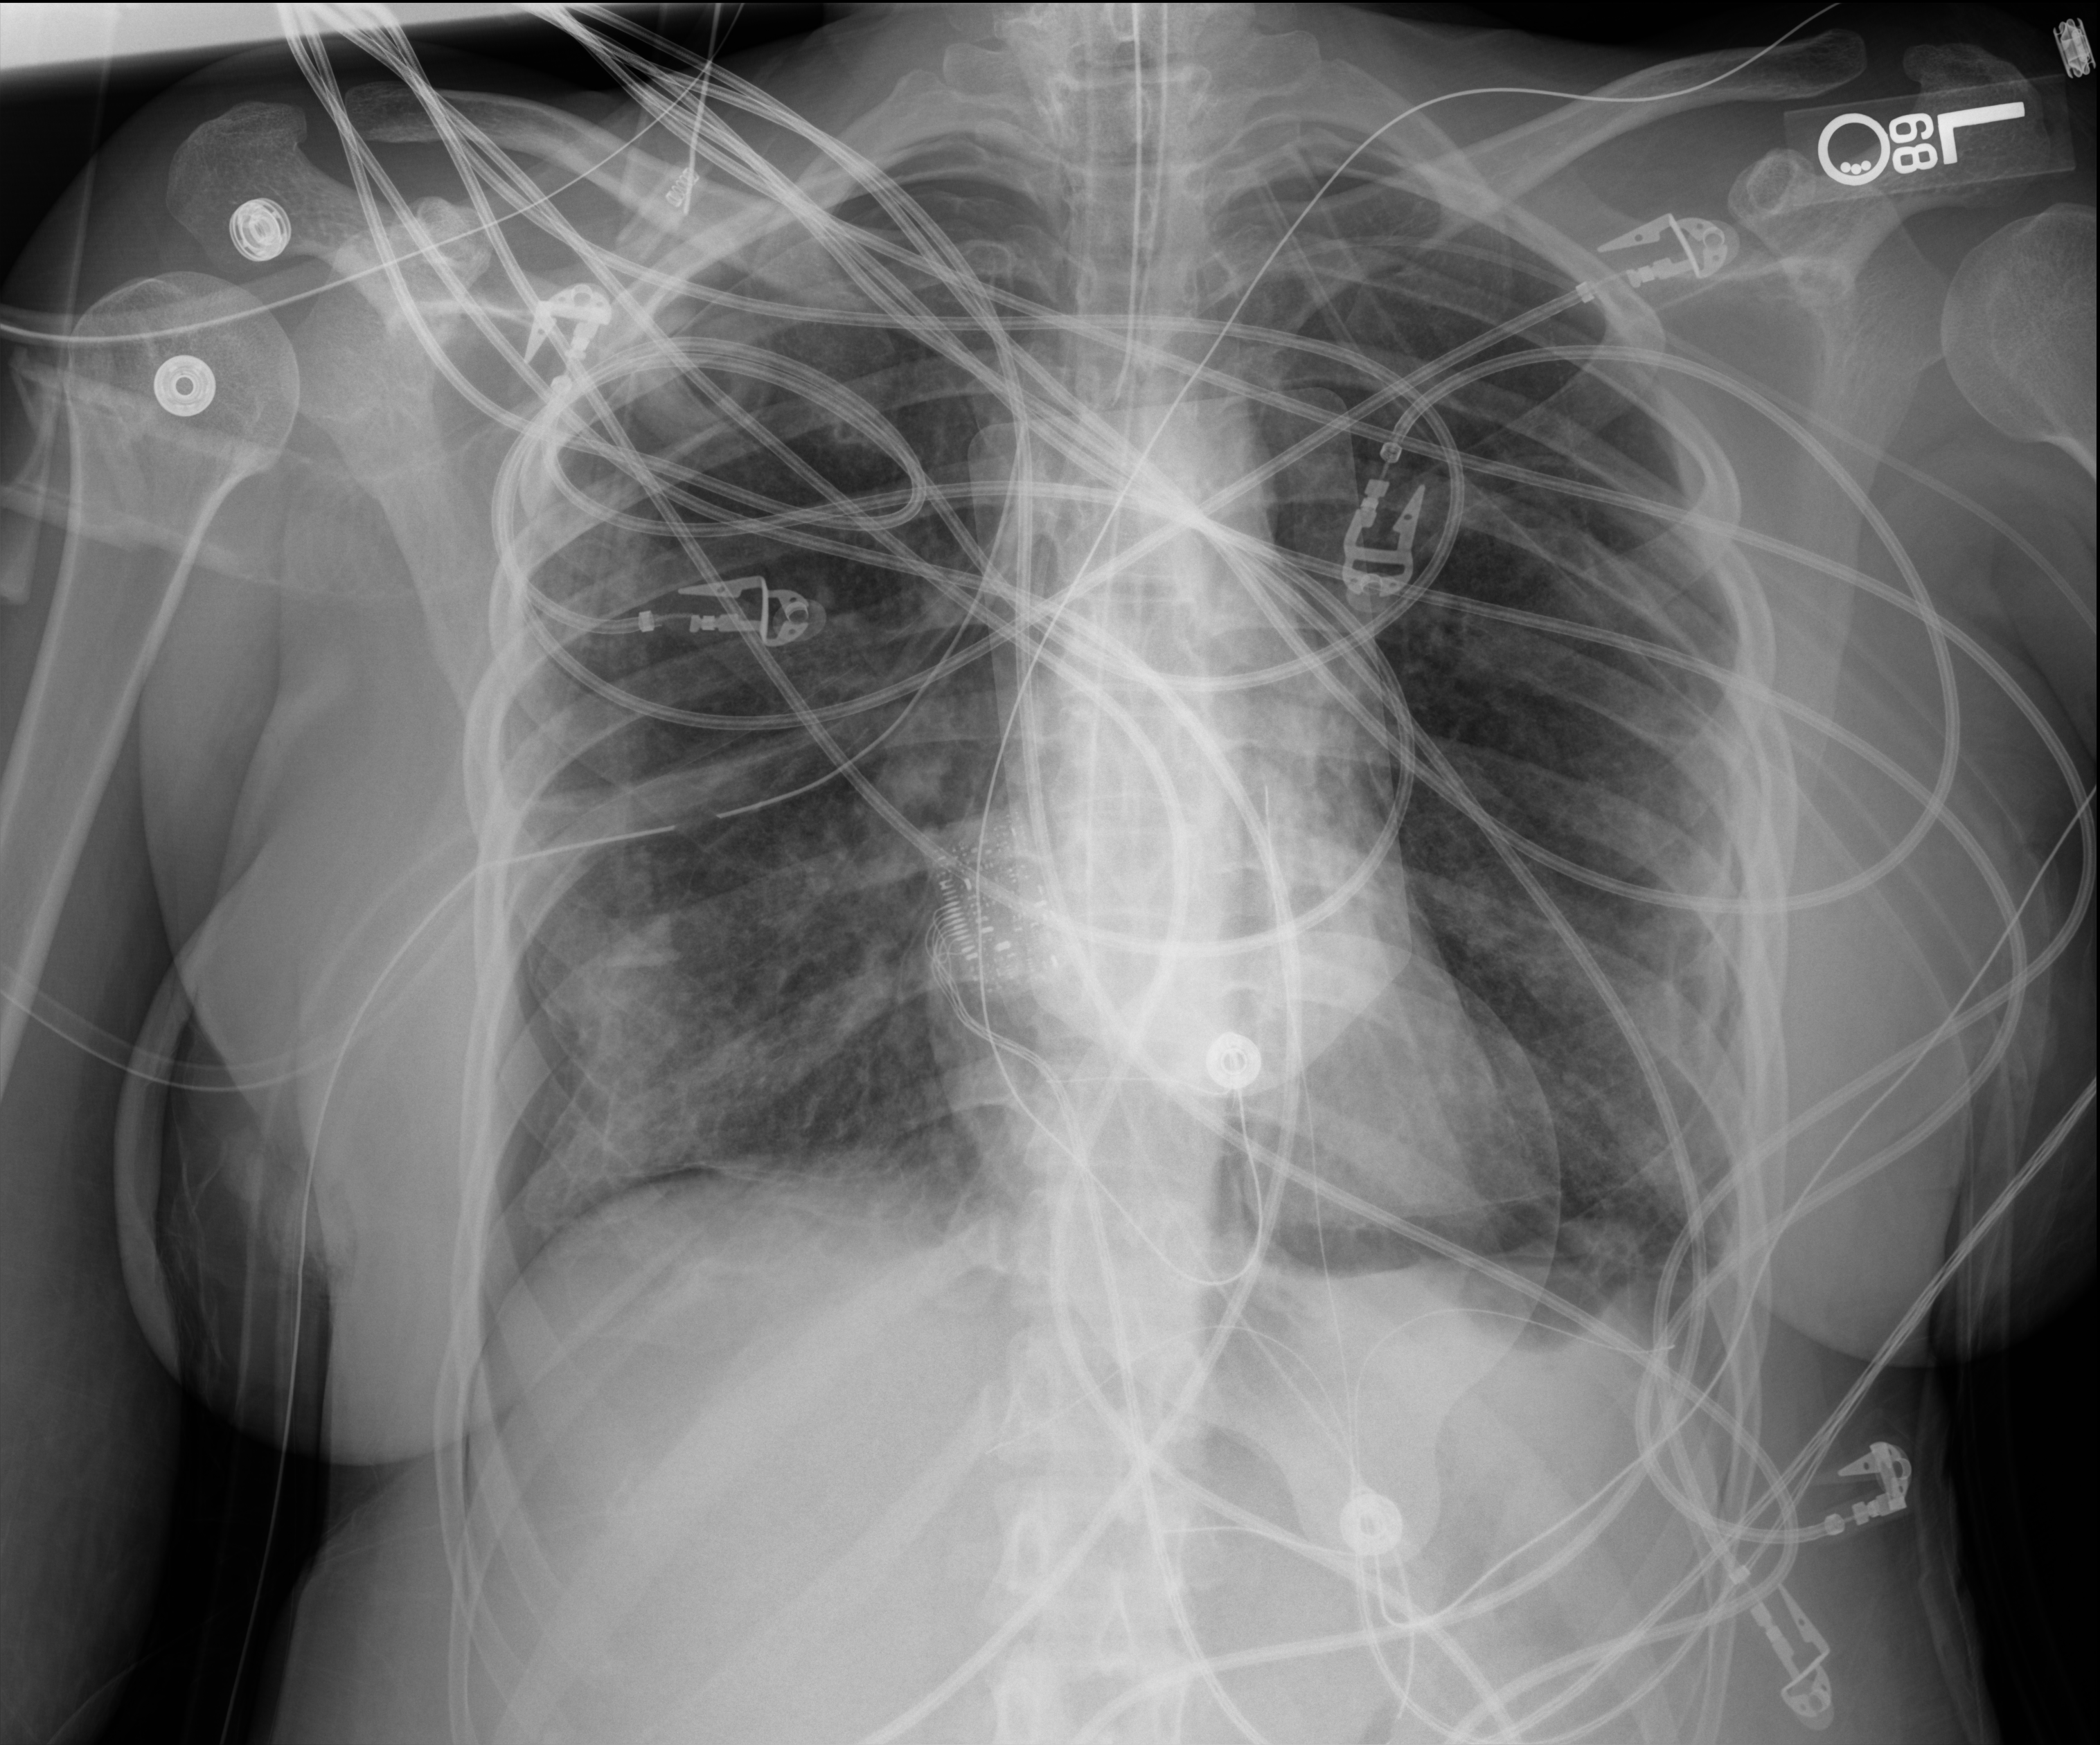
Portable chest radiograph; anteroposterior (AP) projection. Patient hospitalised with COVID-19, aged 18–59 years.
Admission-level facts for this patient (not findings on this image; timing relative to this image not recorded): admitted to intensive care during this hospital stay: yes; mechanically ventilated during this hospital stay: yes; diabetes (admission record): no.